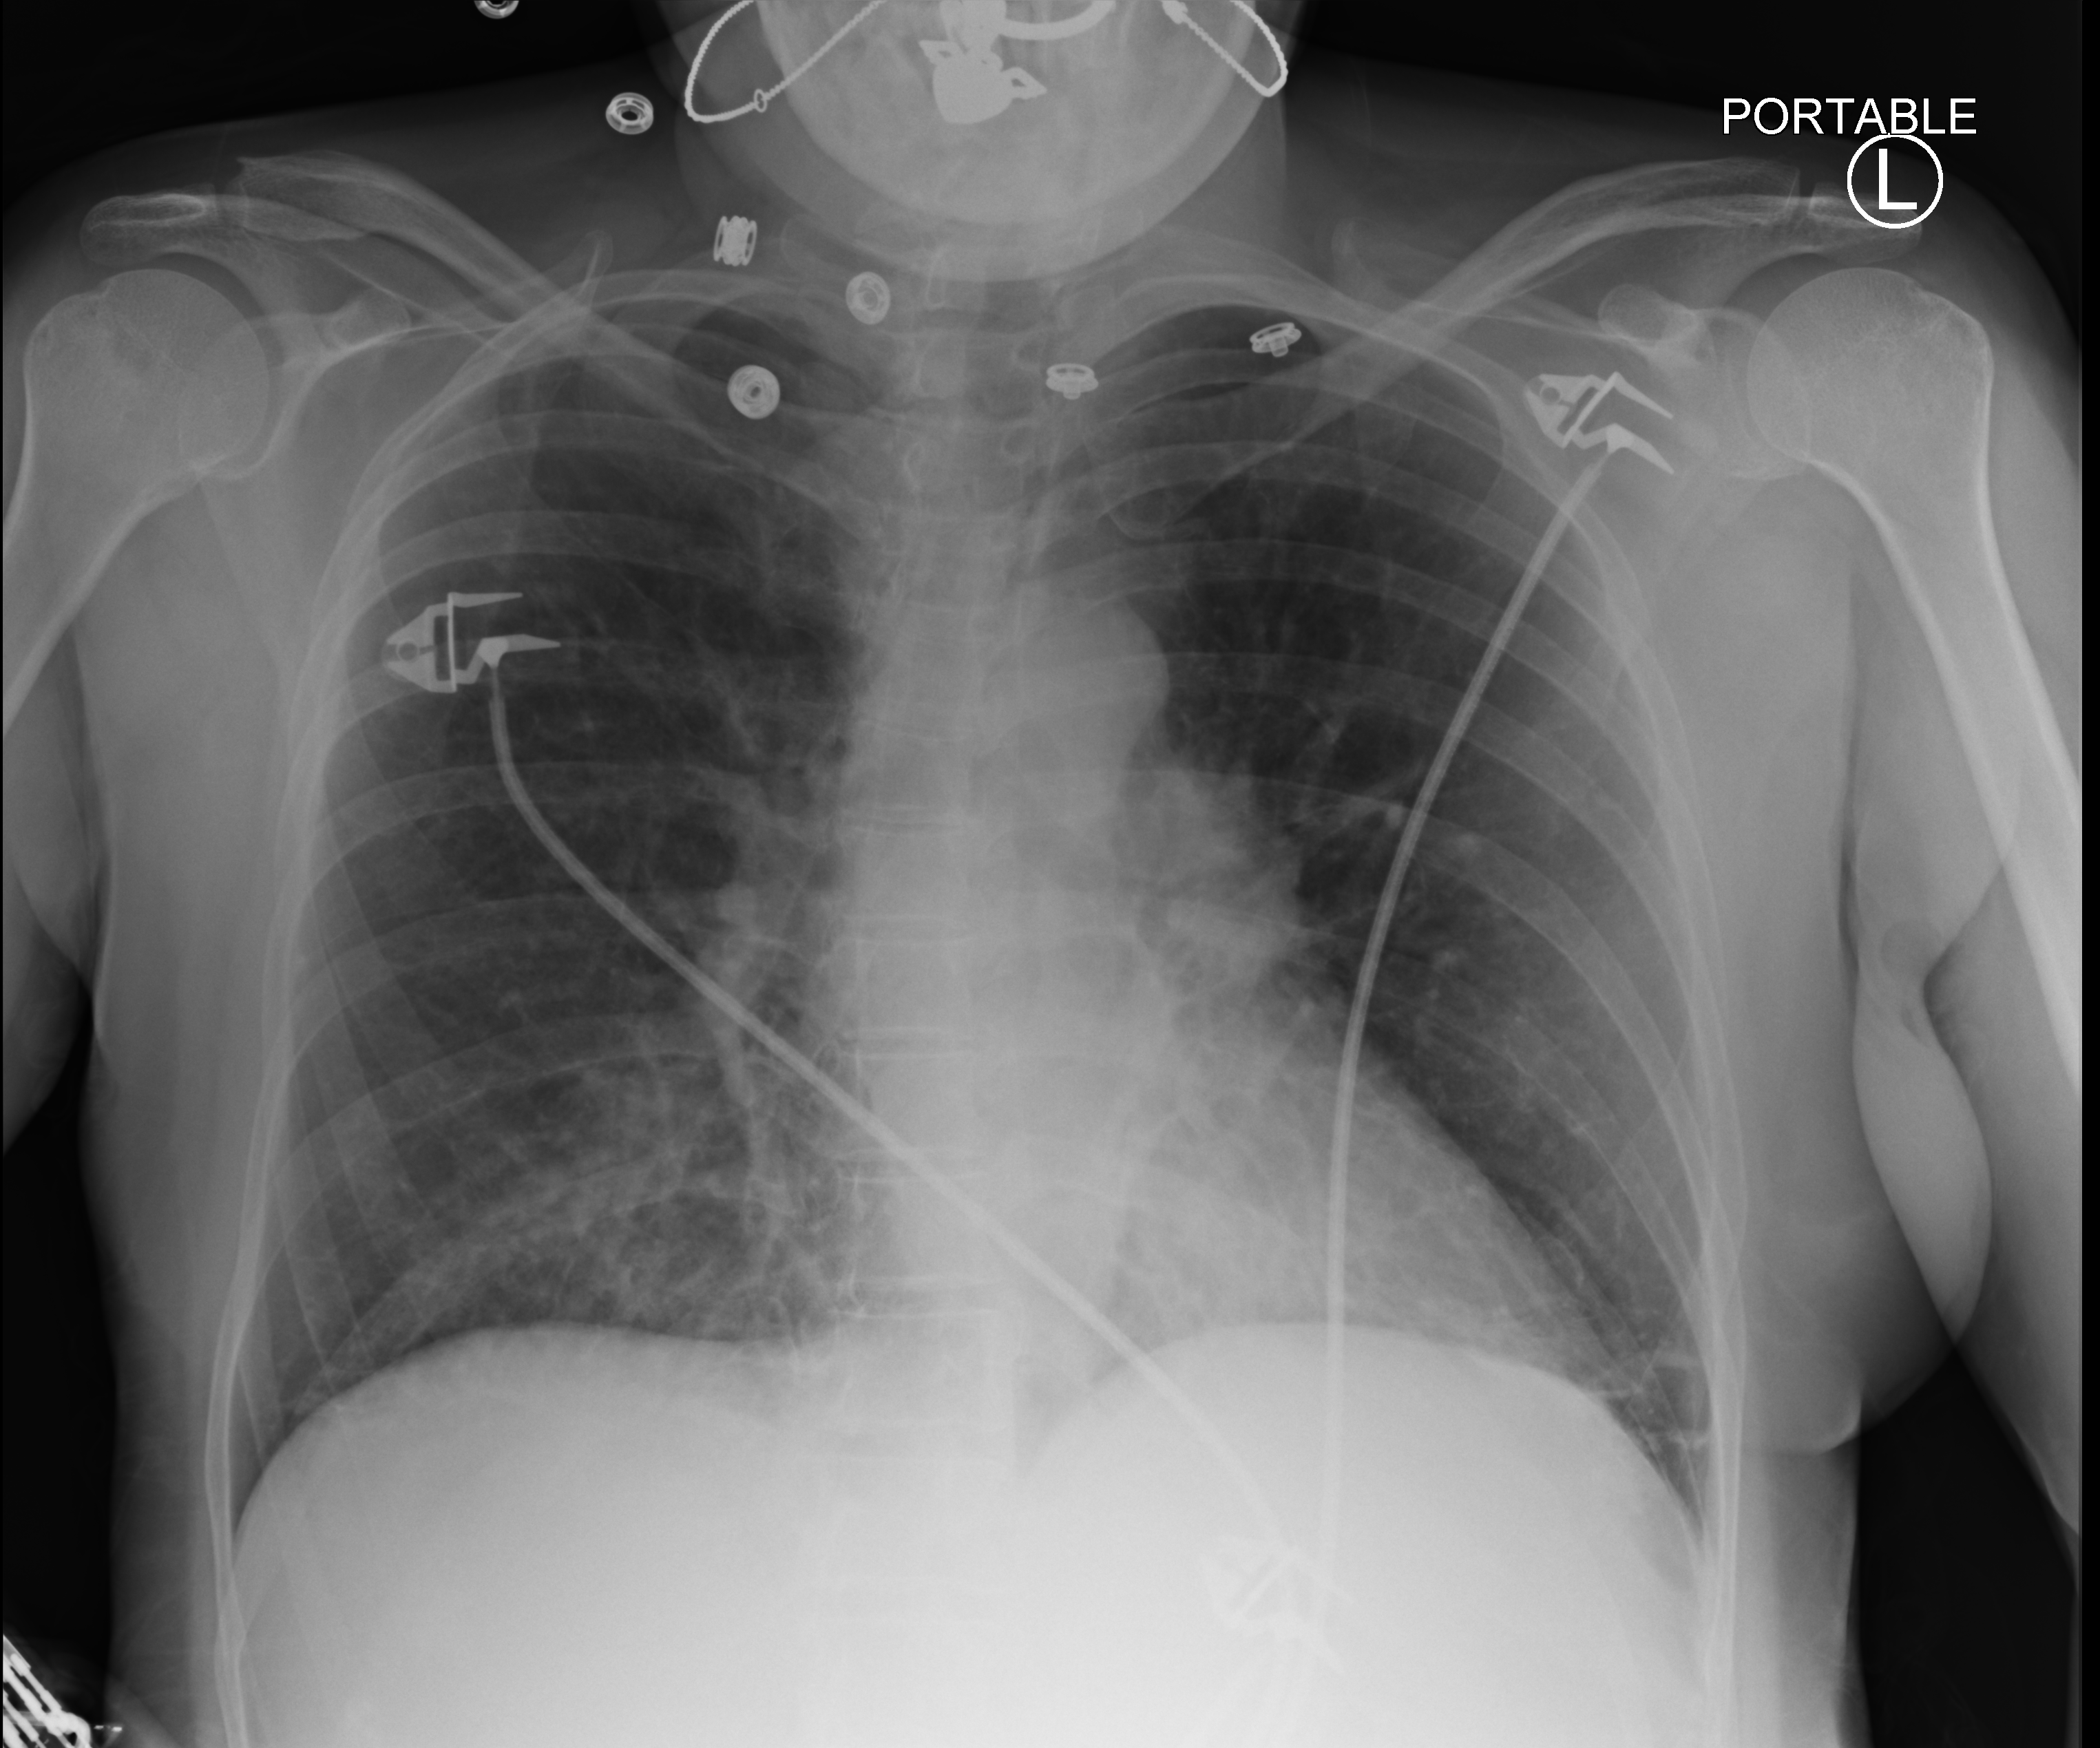
Bedside chest radiograph (computed radiography); anteroposterior (AP) projection. Patient hospitalised with COVID-19; female, aged 18–59 years.
Hospital-stay facts (about this admission, not read from this image; timing relative to this image not recorded): admitted to intensive care during this hospital stay: no.